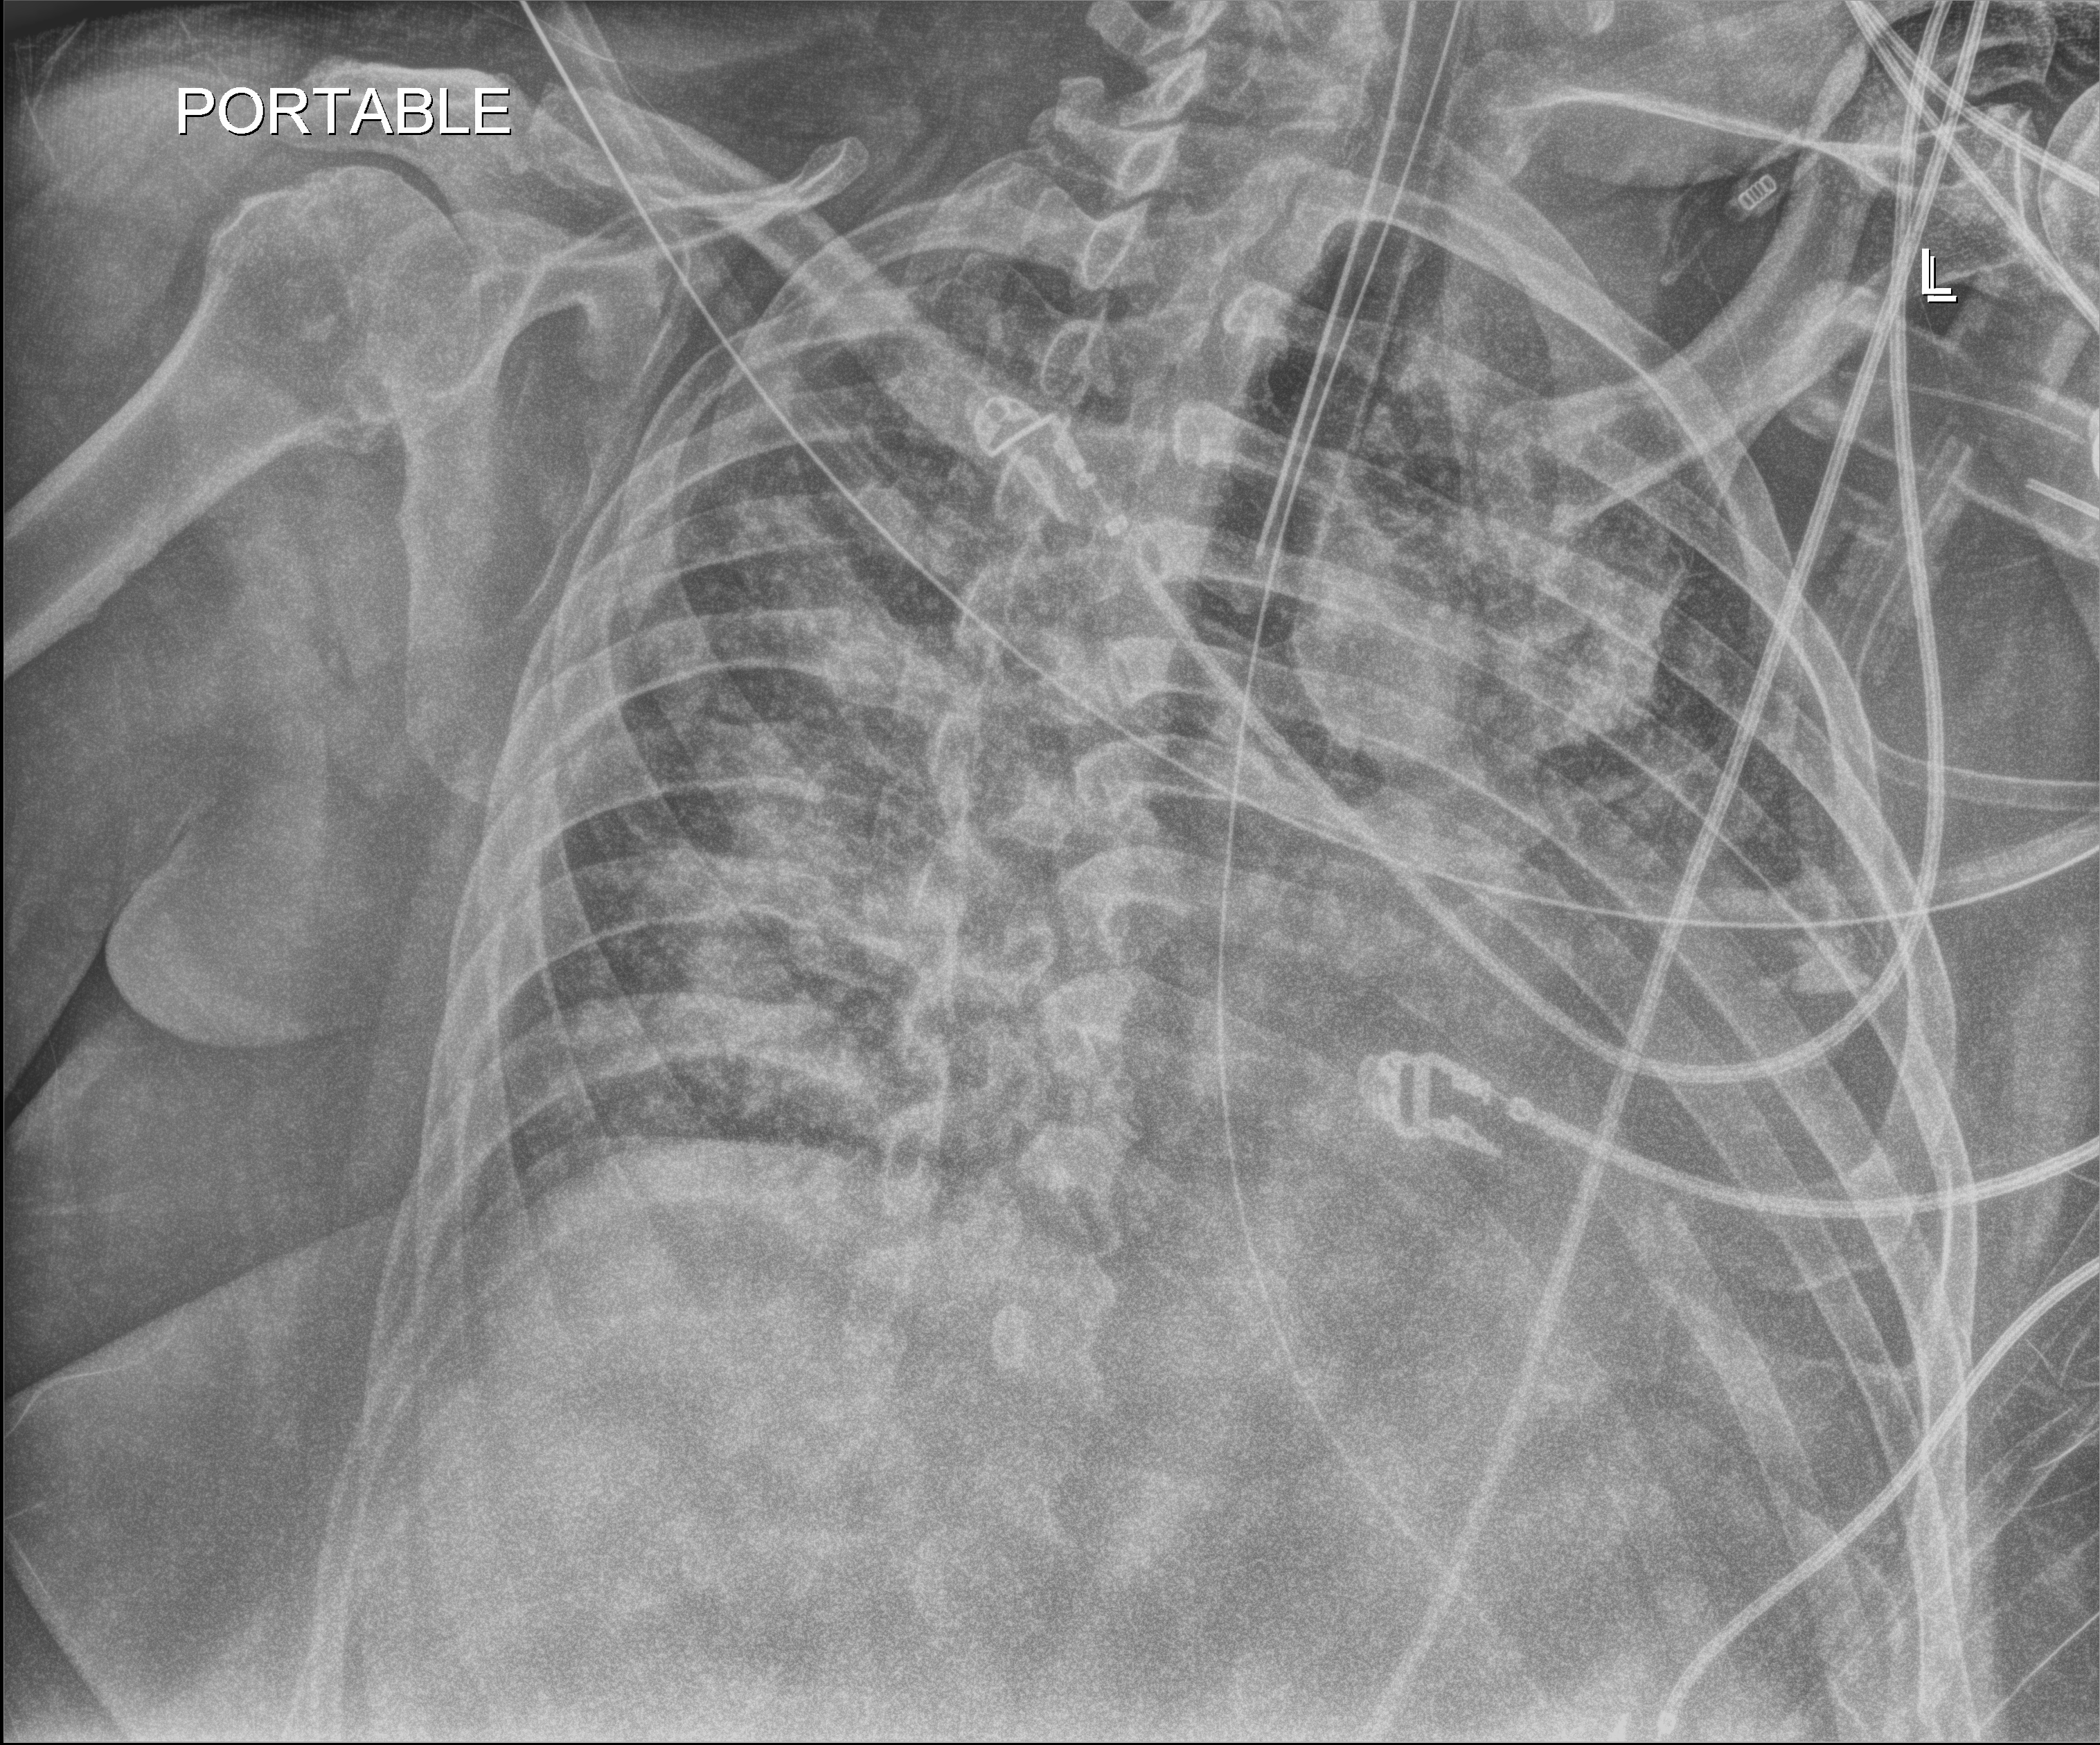
Bedside chest radiograph (digital radiography), anteroposterior (AP) projection. Patient hospitalised with COVID-19; male, aged 18–59 years.
Hospital-stay facts (about this admission, not read from this image; timing relative to this image not recorded):
- hypertension (admission record): yes
- chronic kidney disease (admission record): no